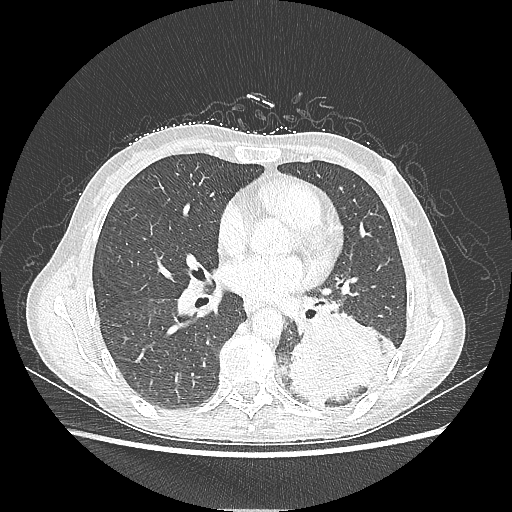
Chest CT, one axial slice; 80 kVp; lung window (W 1500 / L -600 HU); 1.25 mm slice thickness; 512 × 512 image matrix, field of view 360 × 360 mm. Female patient, age 53 years. From the clinical record (not read from this slice): clinical TNM (as recorded): T3 N0 M0.
Annotated regions visible in this slice (rectangle marked by the reading radiologist):
- lung tumour (recorded histology: adenocarcinoma): bounding box [x1, y1, x2, y2] px = [289, 304, 399, 409]